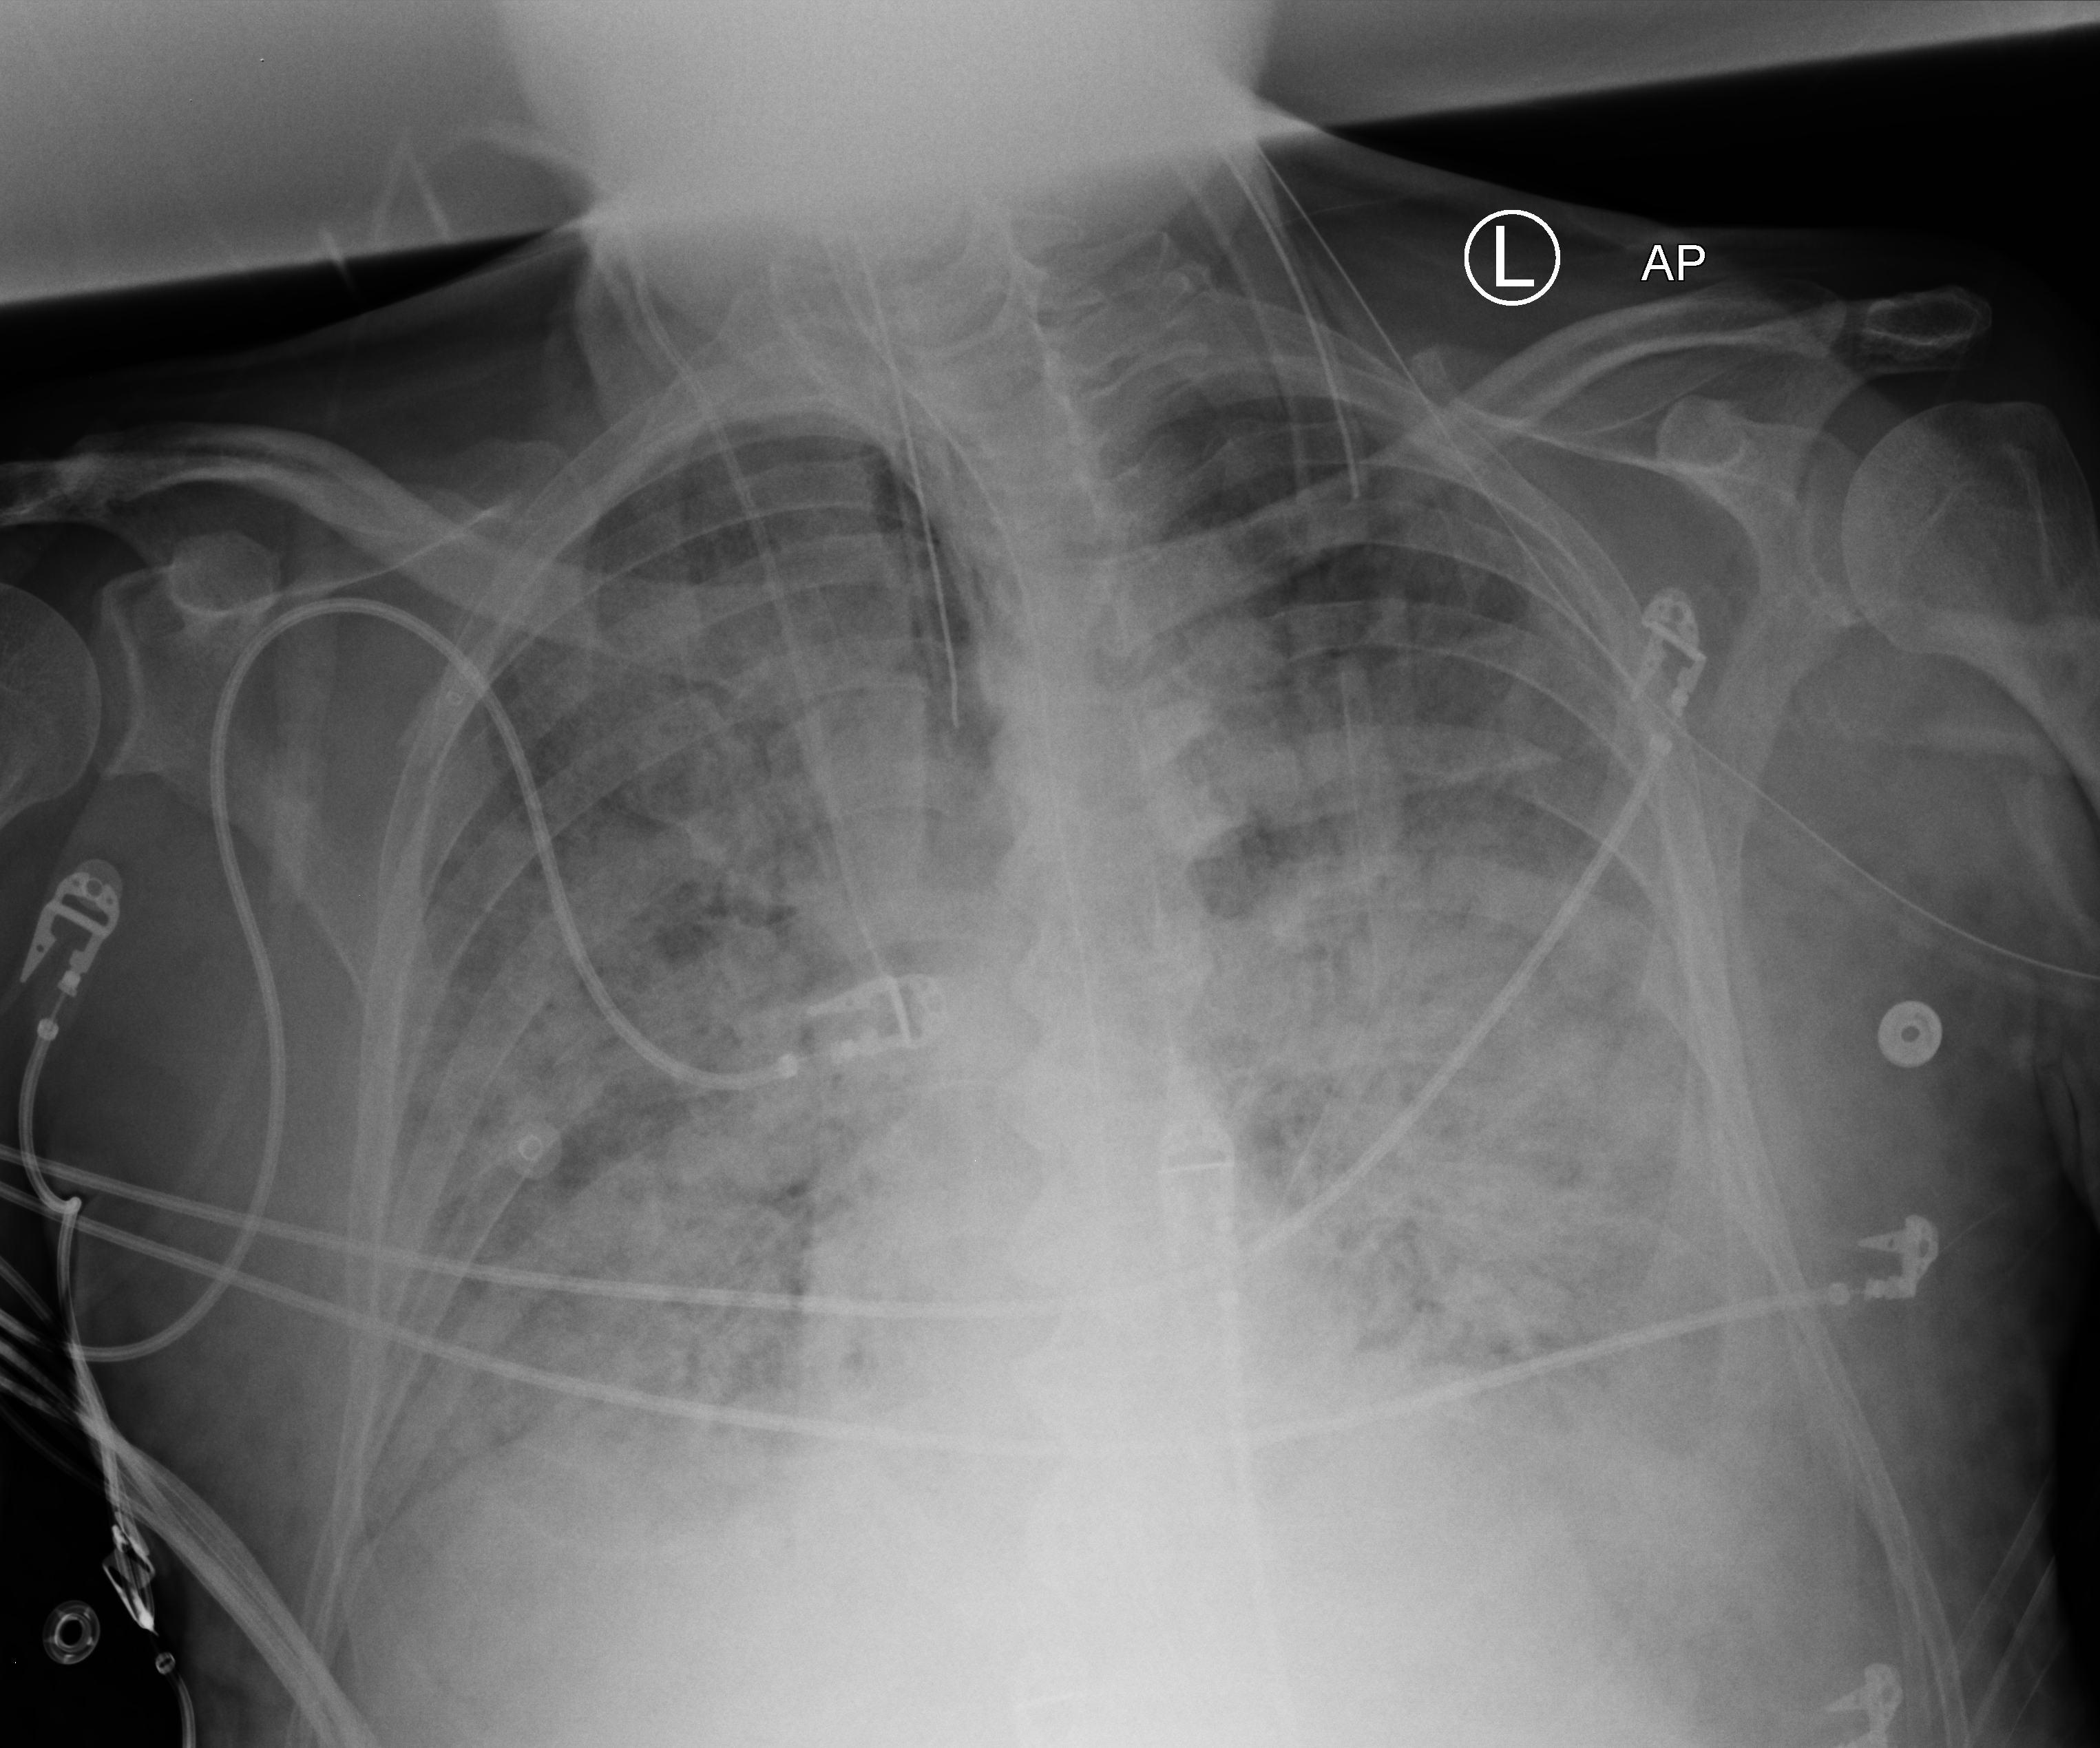
Portable chest radiograph, anteroposterior (AP) projection. Male patient hospitalised with COVID-19, age 60–74 years.
Admission-level facts for this patient (not findings on this image; timing relative to this image not recorded): other chronic lung disease (admission record): no.